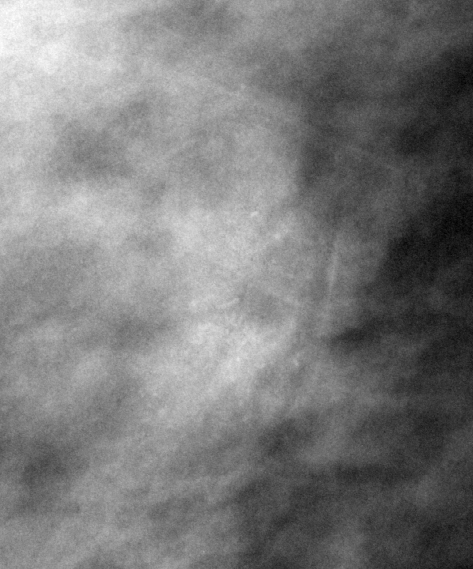
Crop from a digitized film mammogram around one marked abnormality; right breast; MLO view.
Finding: calcifications, morphology amorphous, distribution clustered; BI-RADS assessment category 4; pathology (as recorded): benign.